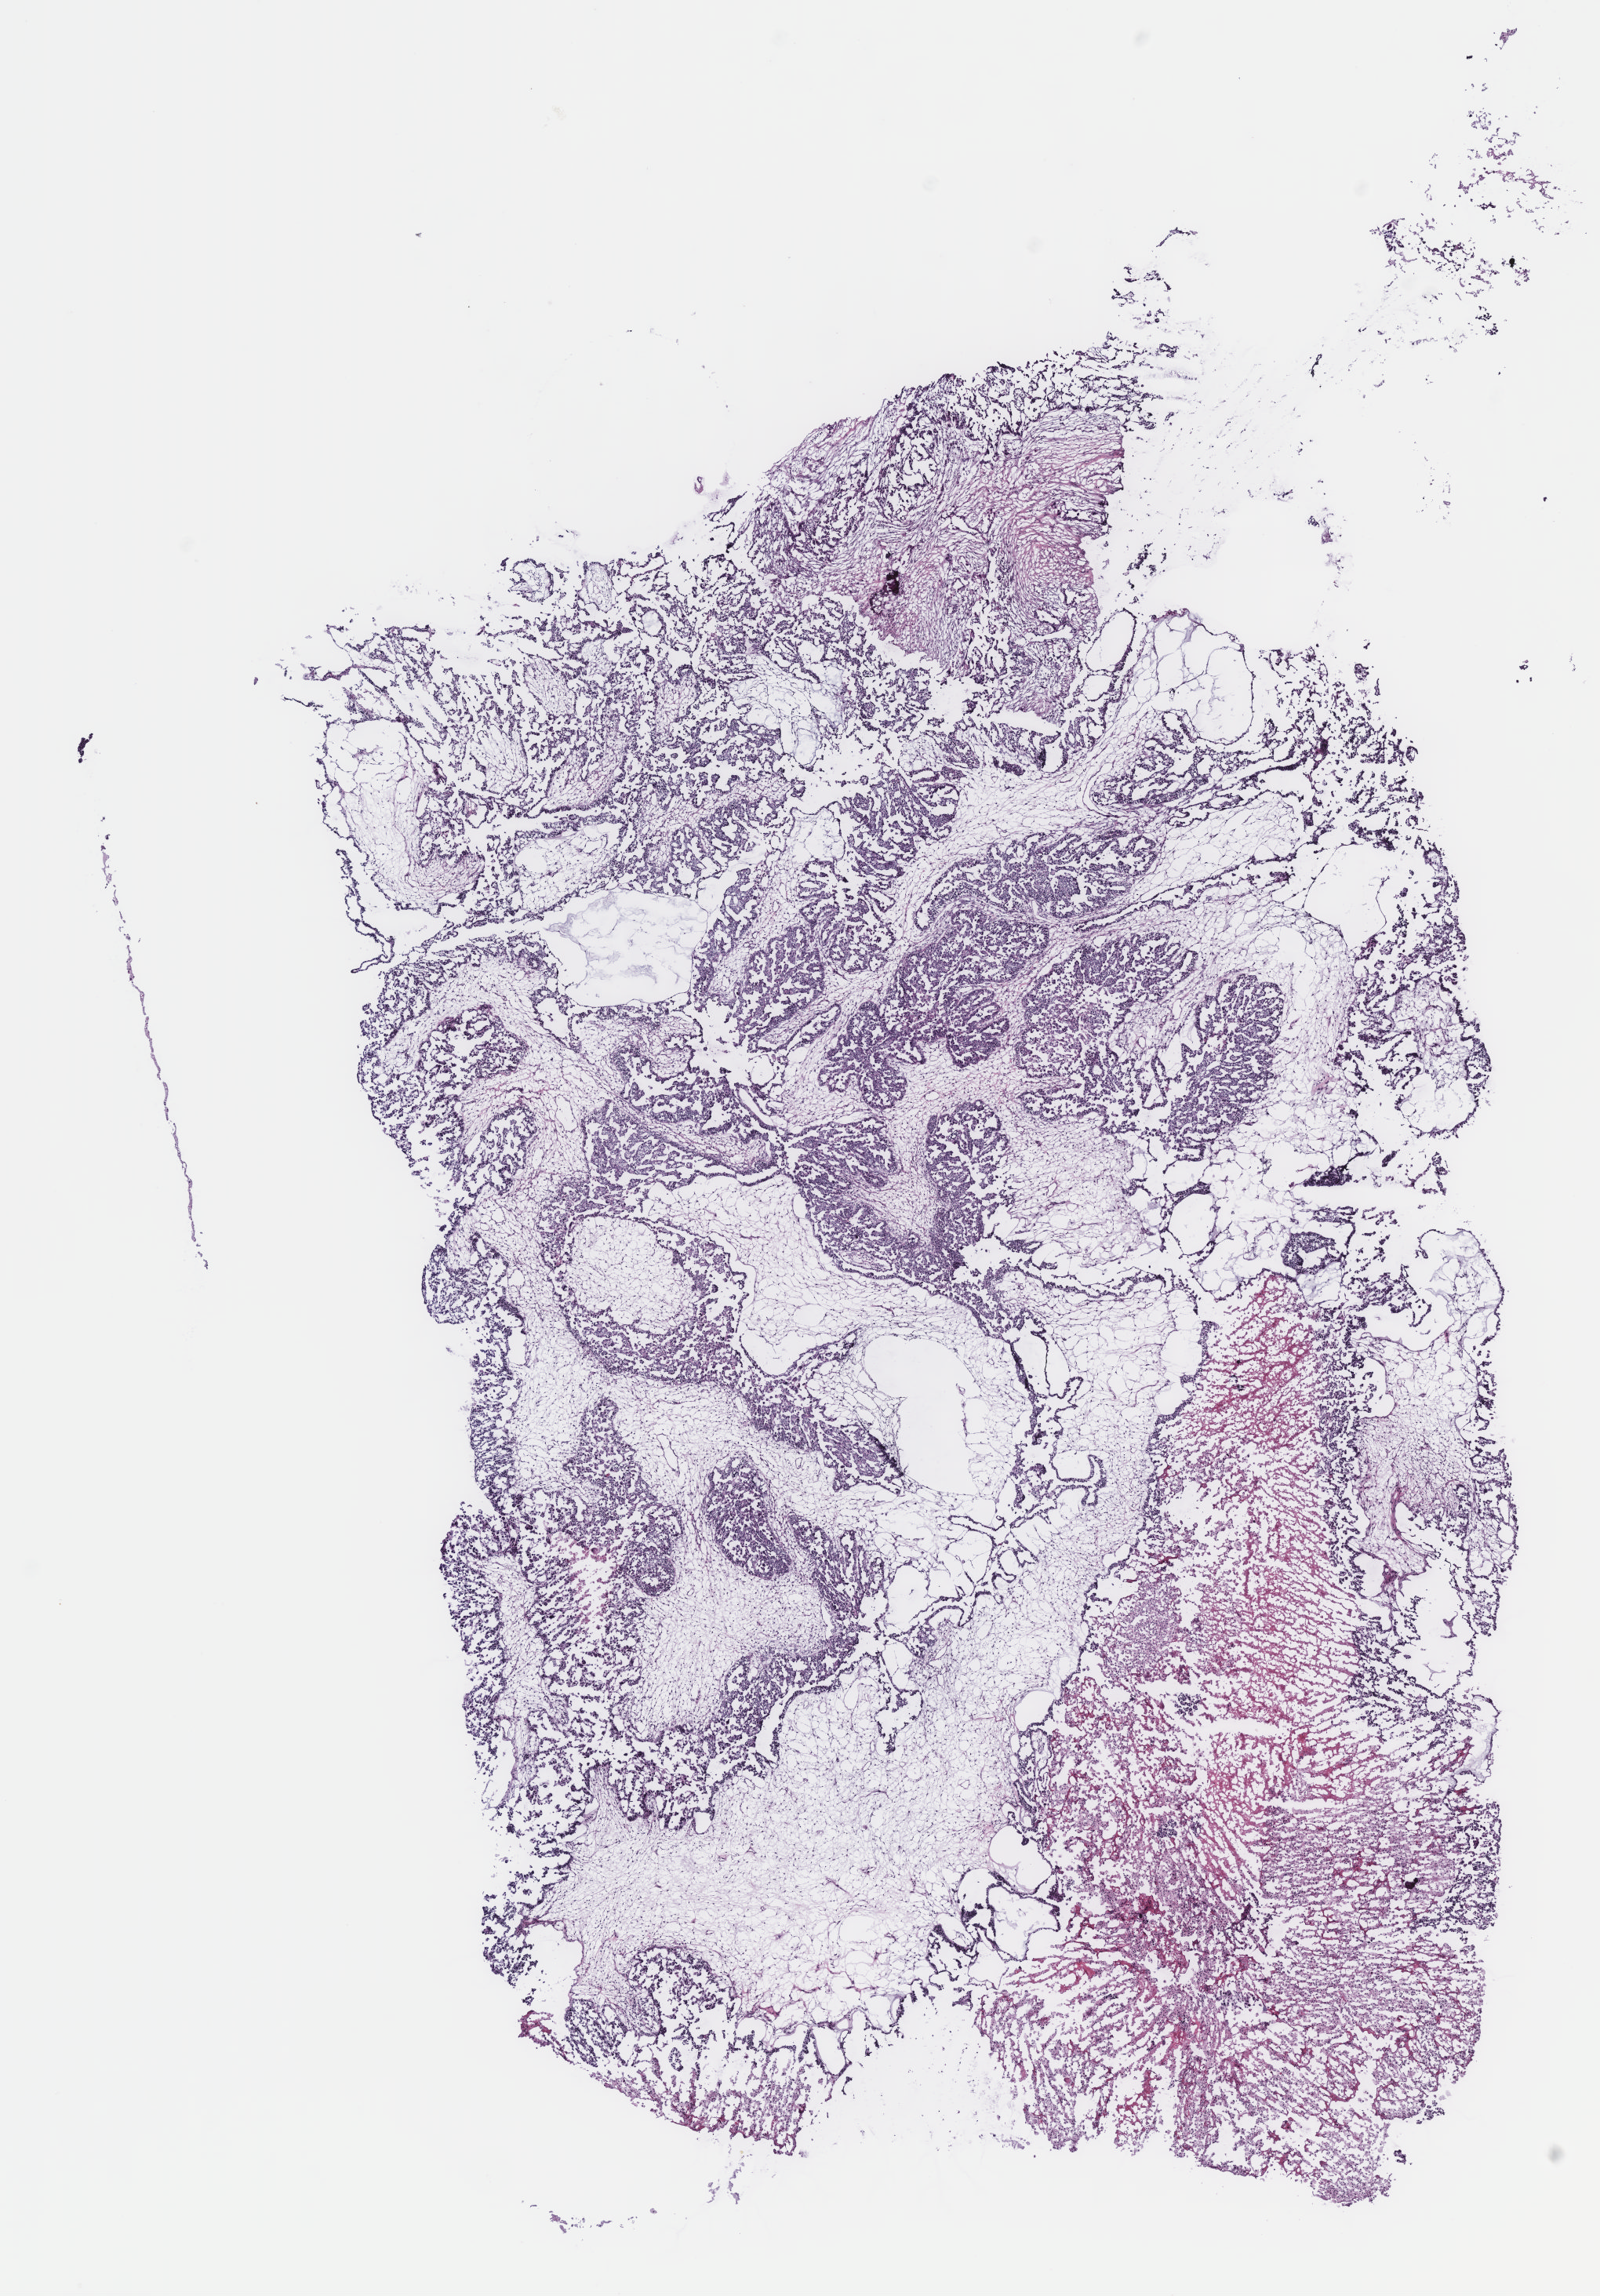
Digitized H&E-stained tissue section (whole slide) — shown as a low-resolution overview of the whole scanned area (about 8.2 x 11.7 mm). Ovary, tumour tissue. Patient: female, age 68 years.
Histologic diagnosis: Serous adenocarcinoma, NOS. Primary tumour site (as recorded): ovary.